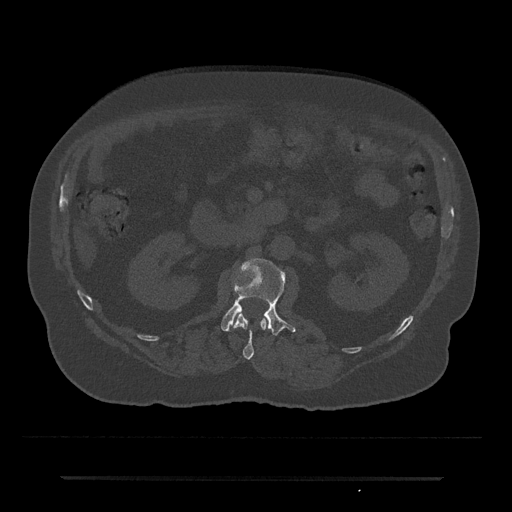
CT including the spine, one axial slice; position 32 of 797 along the scan axis; reconstruction kernel Br40s/3; bone window (W 1800 / L 400 HU); 0.5 mm slice thickness; 512 × 512 image matrix, field of view 437 × 437 mm. Patient: male, 69 years. From the clinical record (not read from this slice): primary cancer: prostate.
Annotated regions visible in this slice (semi-automatically segmented with operator editing):
- L1 vertebra: box from (x=233, y=313) to (x=267, y=359) px
- L2 vertebra: (x=221, y=258)–(x=296, y=336)